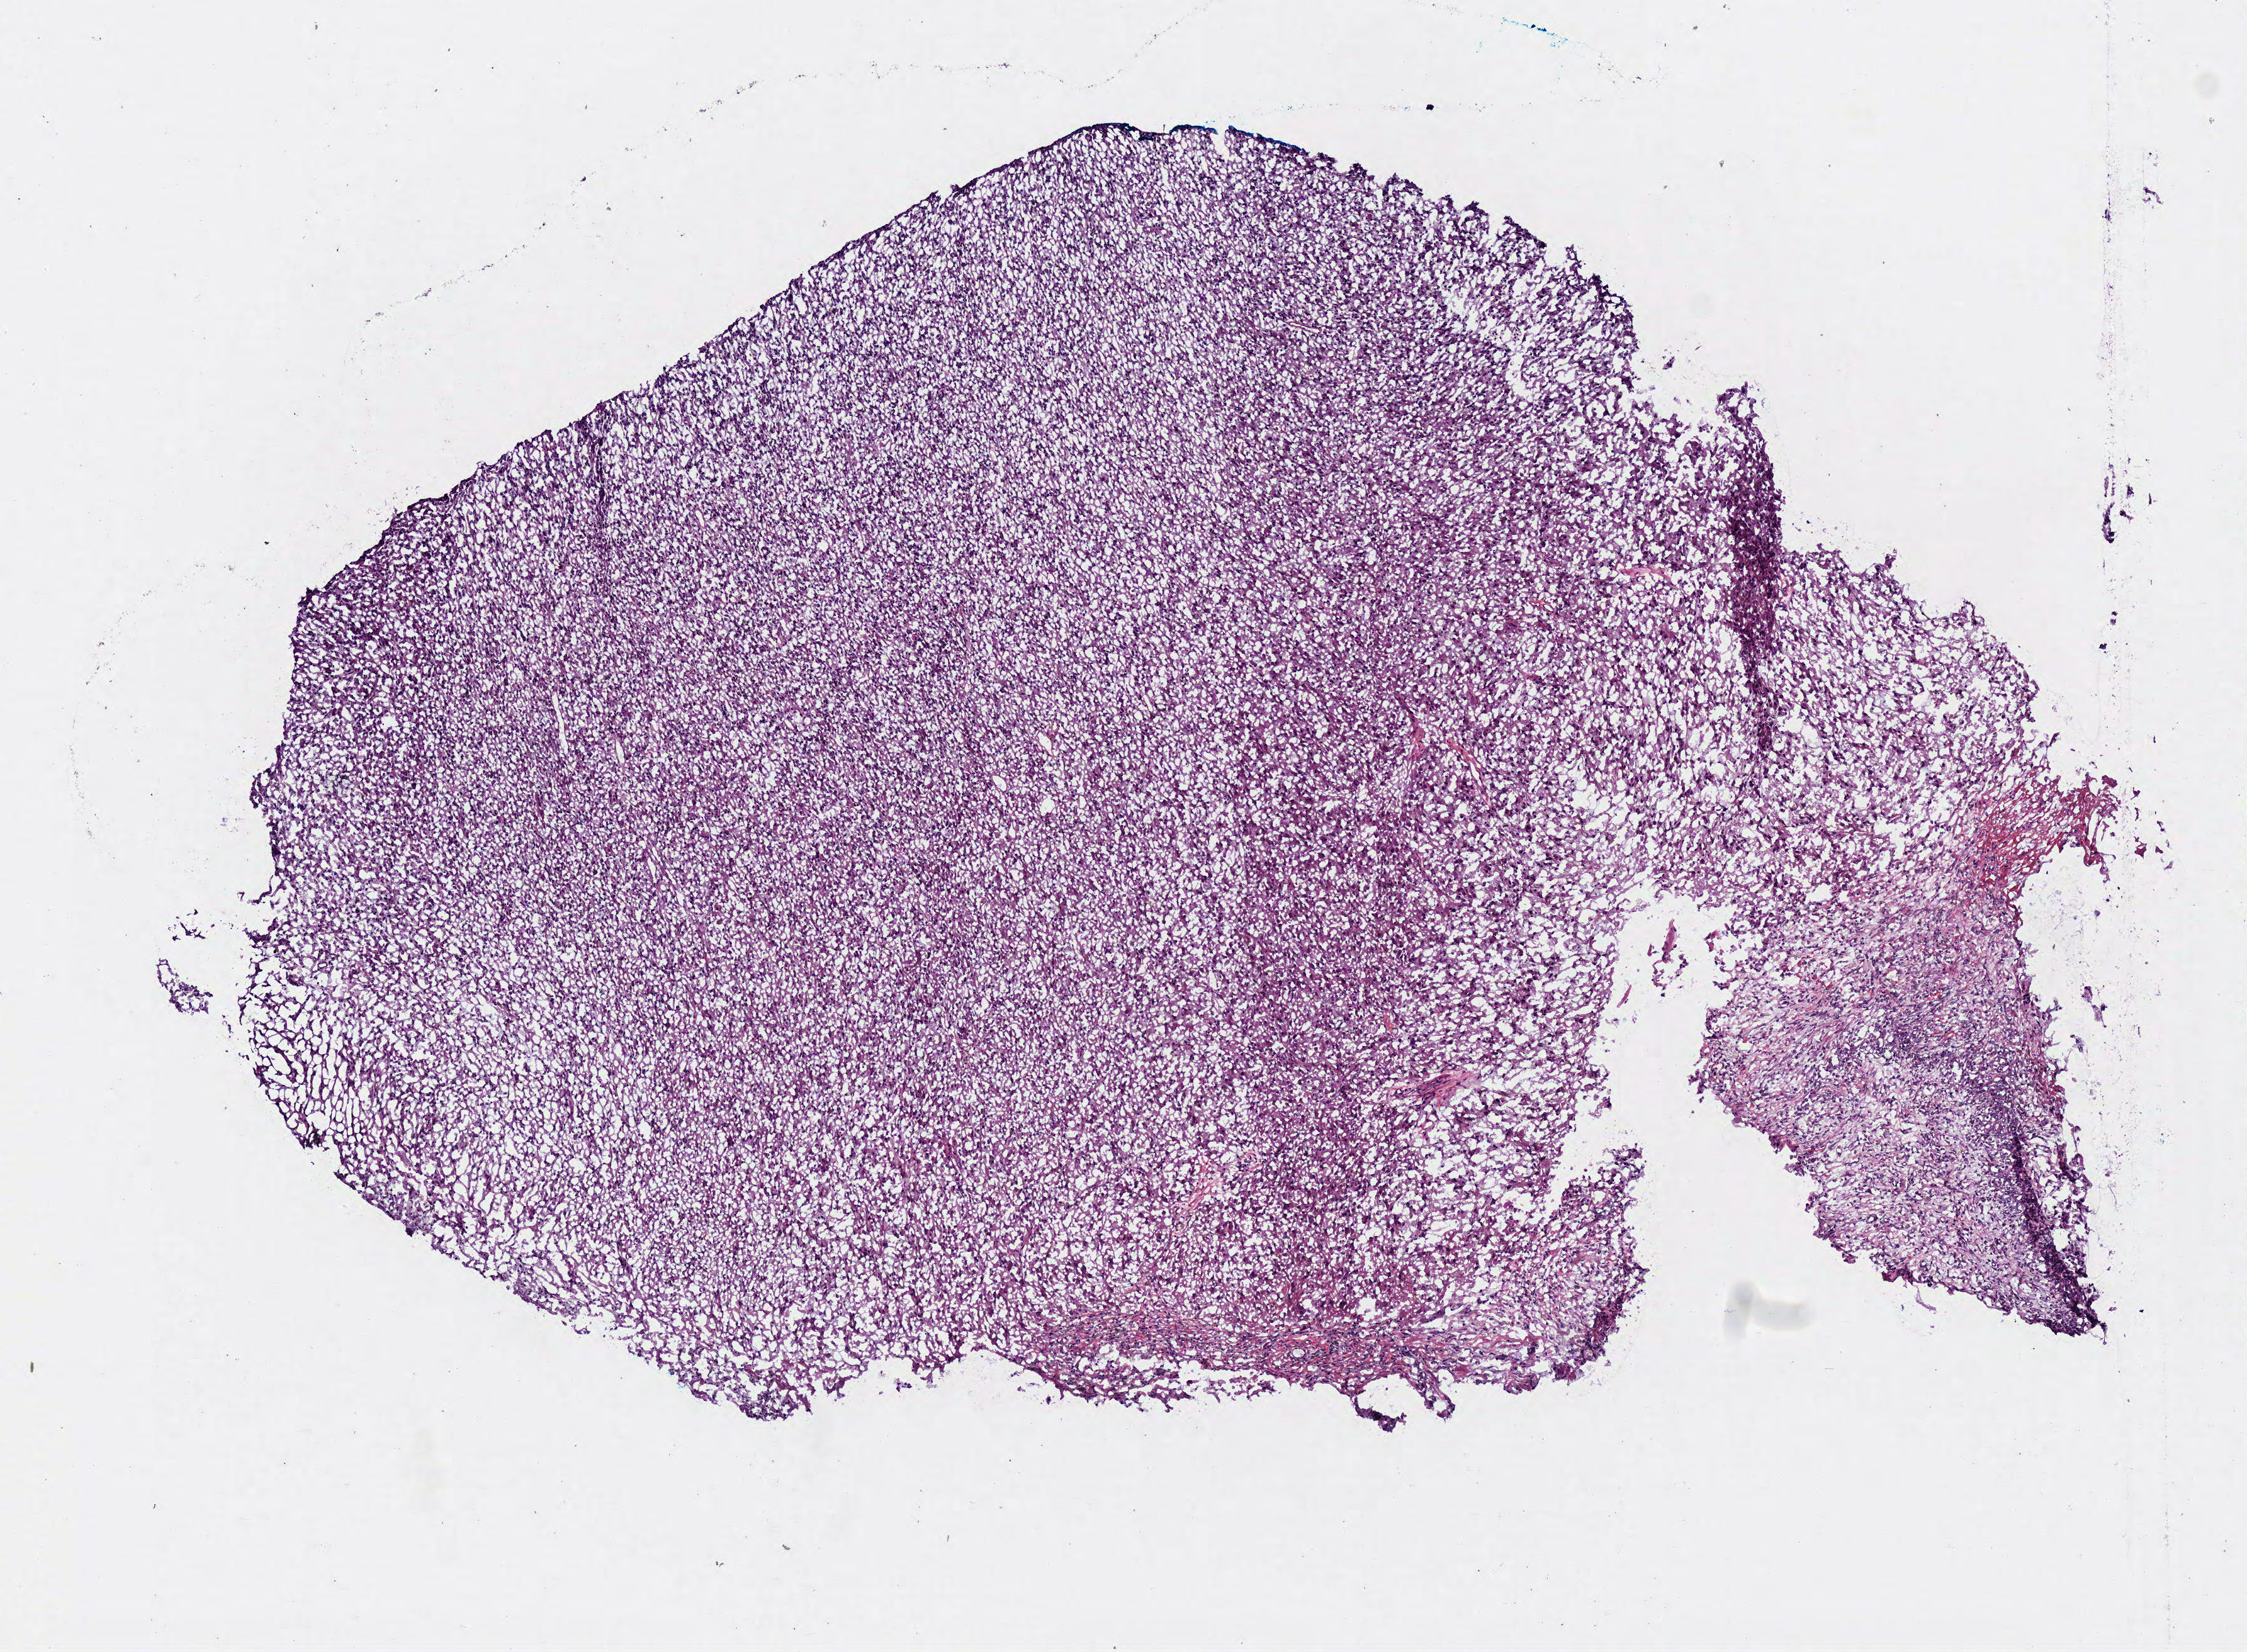
Whole-slide histology image, Hematoxylin and eosin (H&E) stained — shown as a low-resolution overview of the whole scanned area (about 7.0 x 5.2 mm, from a 40x scan). Frozen section from the bottom of the tissue portion. Brain, primary tumour sample. Patient: female, age at initial diagnosis 77 years. Pathologist review of this section (percent, as recorded): tumour cells 100%, tumour nuclei 80%, normal cells 0%, stromal cells 0%, necrosis 0%.
• histologic diagnosis: Glioblastoma